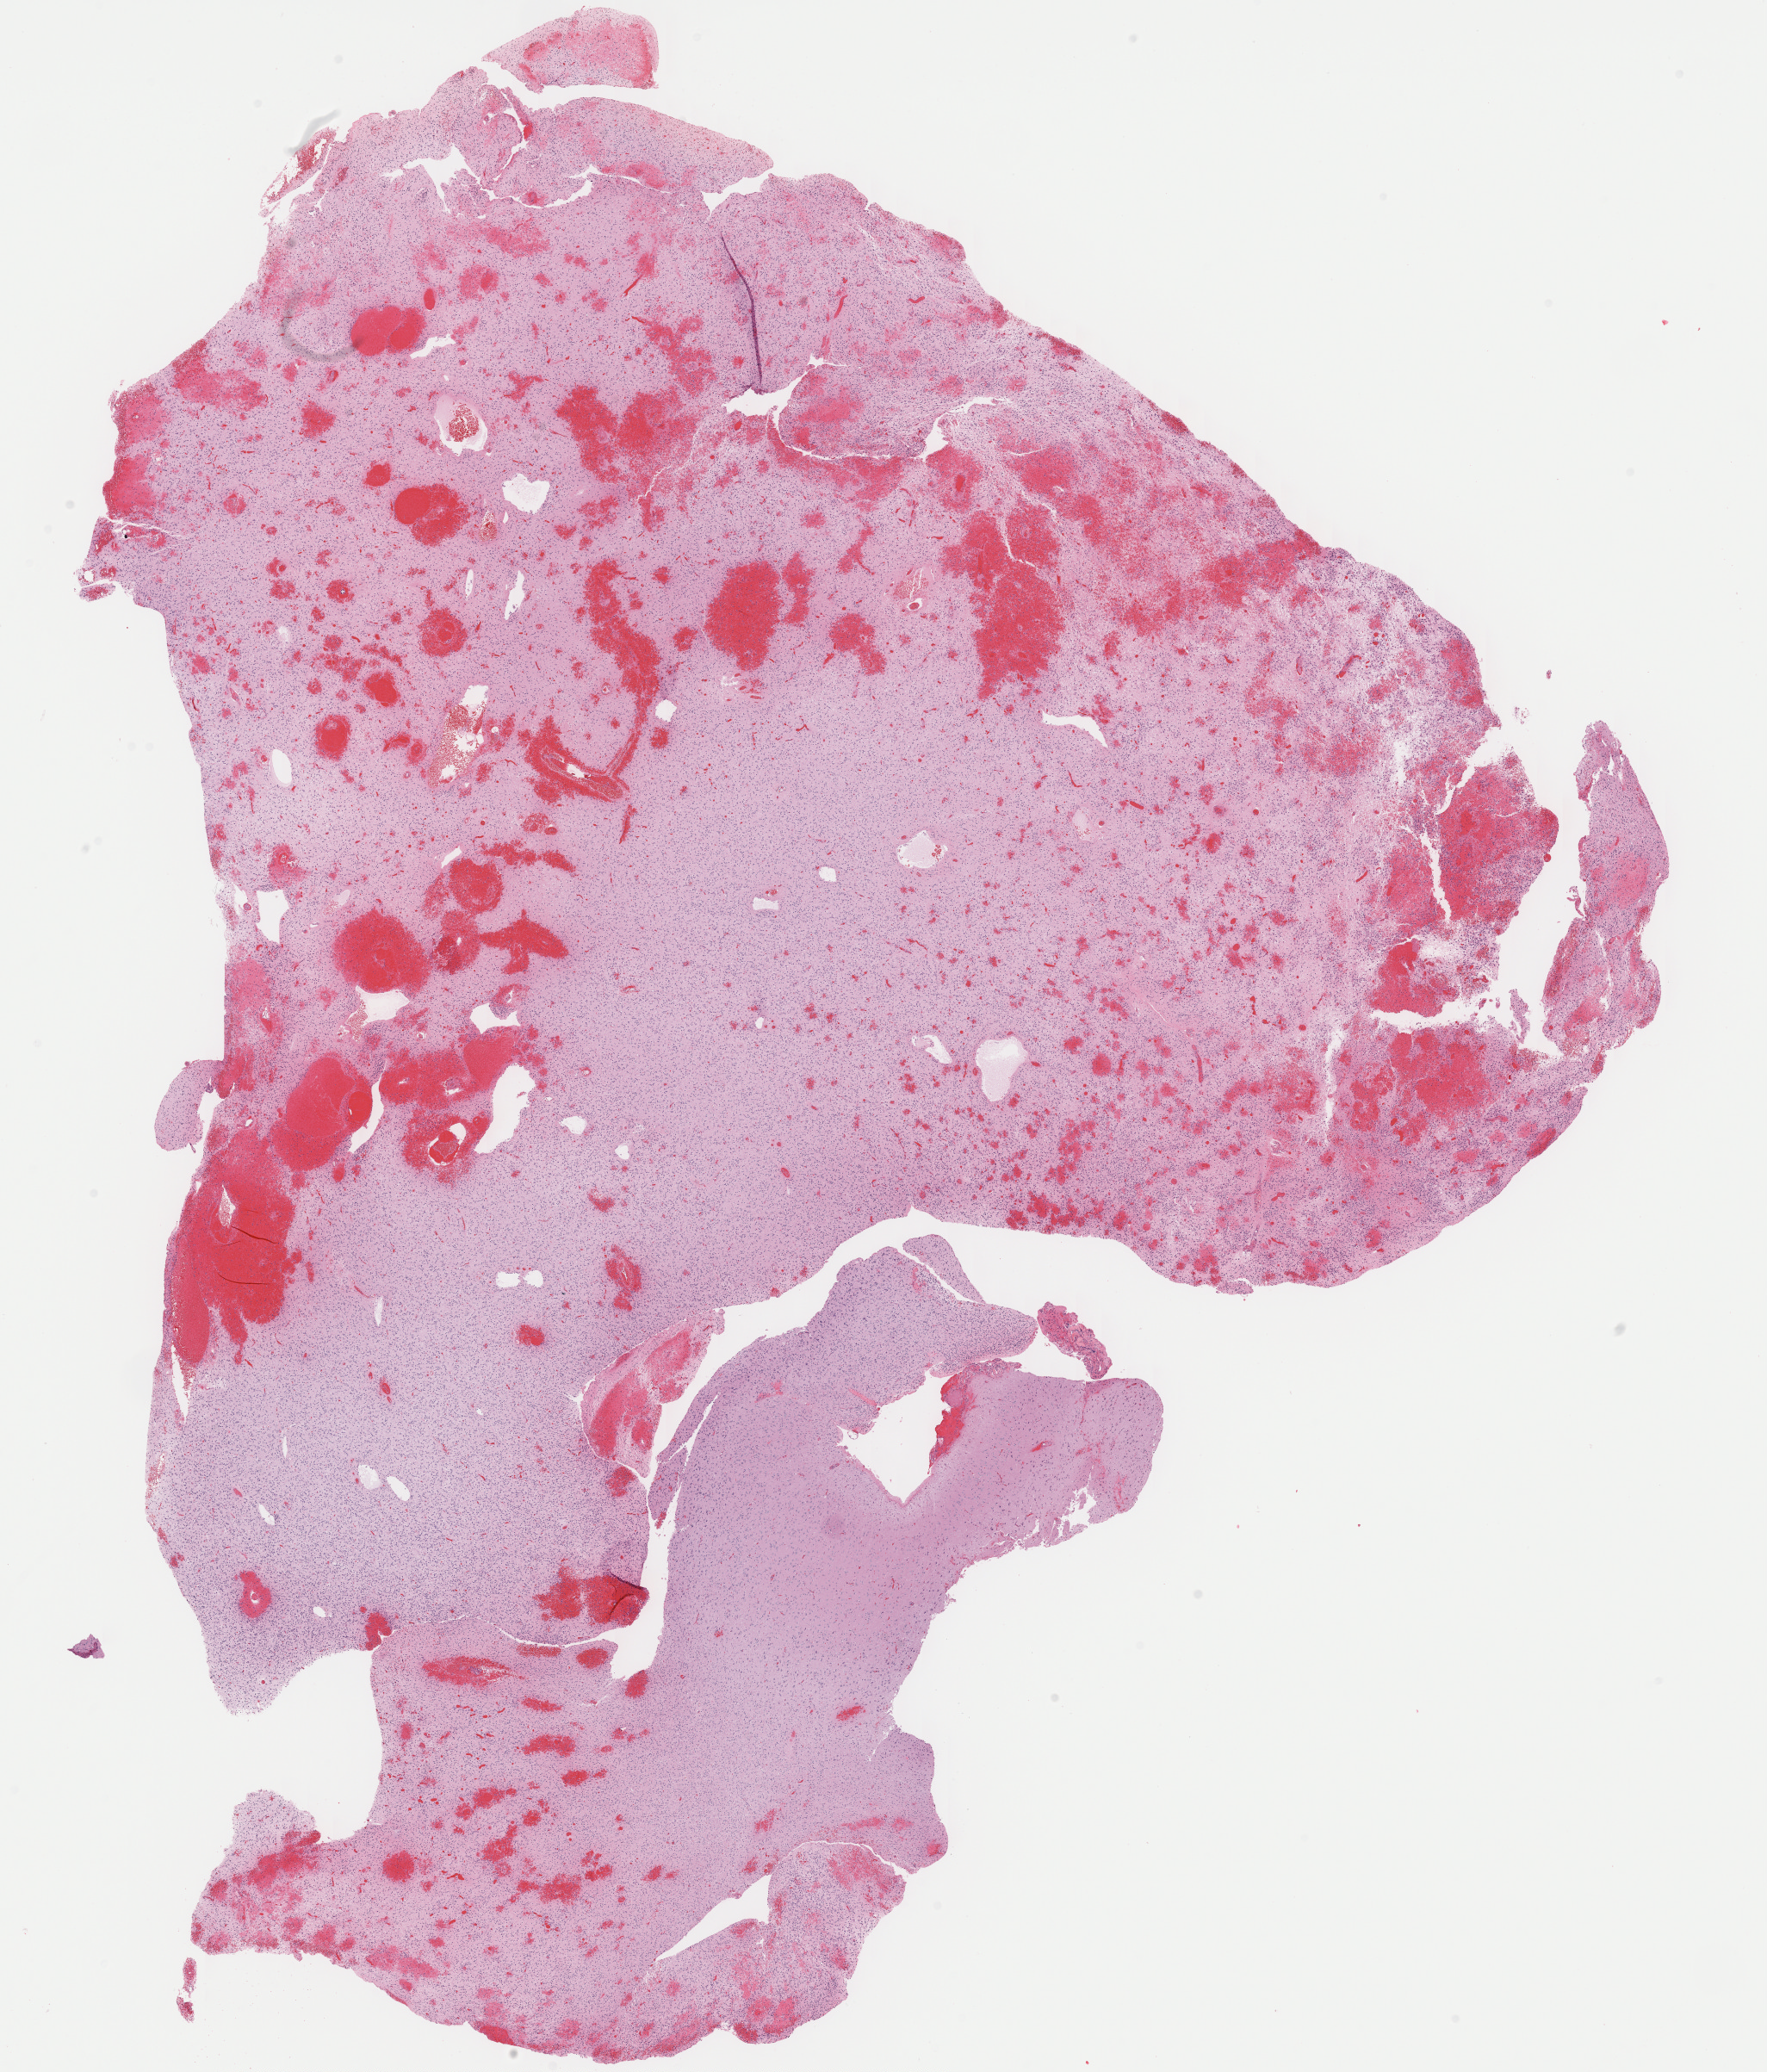
Digitized H&E-stained tissue section (whole slide) — shown as a low-resolution overview of the whole scanned area (about 16.2 x 19.0 mm); formalin-fixed paraffin-embedded (FFPE) diagnostic section; brain, primary tumour sample. Male, age 59 years at initial diagnosis. Histologic grade: G2 (moderately differentiated).
Laterality: right. Histologic diagnosis: Oligodendroglioma, NOS (cerebrum).